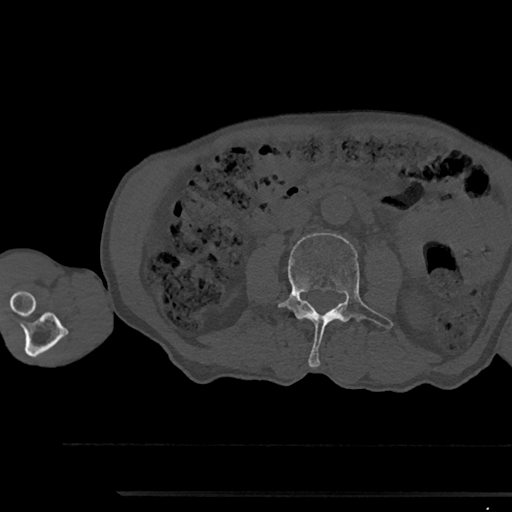
CT including the spine, one axial slice. Slice 492 of 797 in the series (ordered by position). 120 kVp. Bone window (W 1800 / L 400 HU). 0.5 mm slice thickness. 512 × 512 image matrix, field of view 367 × 367 mm. Patient: male, 79 years. From the clinical record (not read from this slice): primary cancer: prostate.
Annotated regions visible in this slice (semi-automatically segmented with operator editing):
- L3 vertebra: box from (x=279, y=233) to (x=393, y=367) px